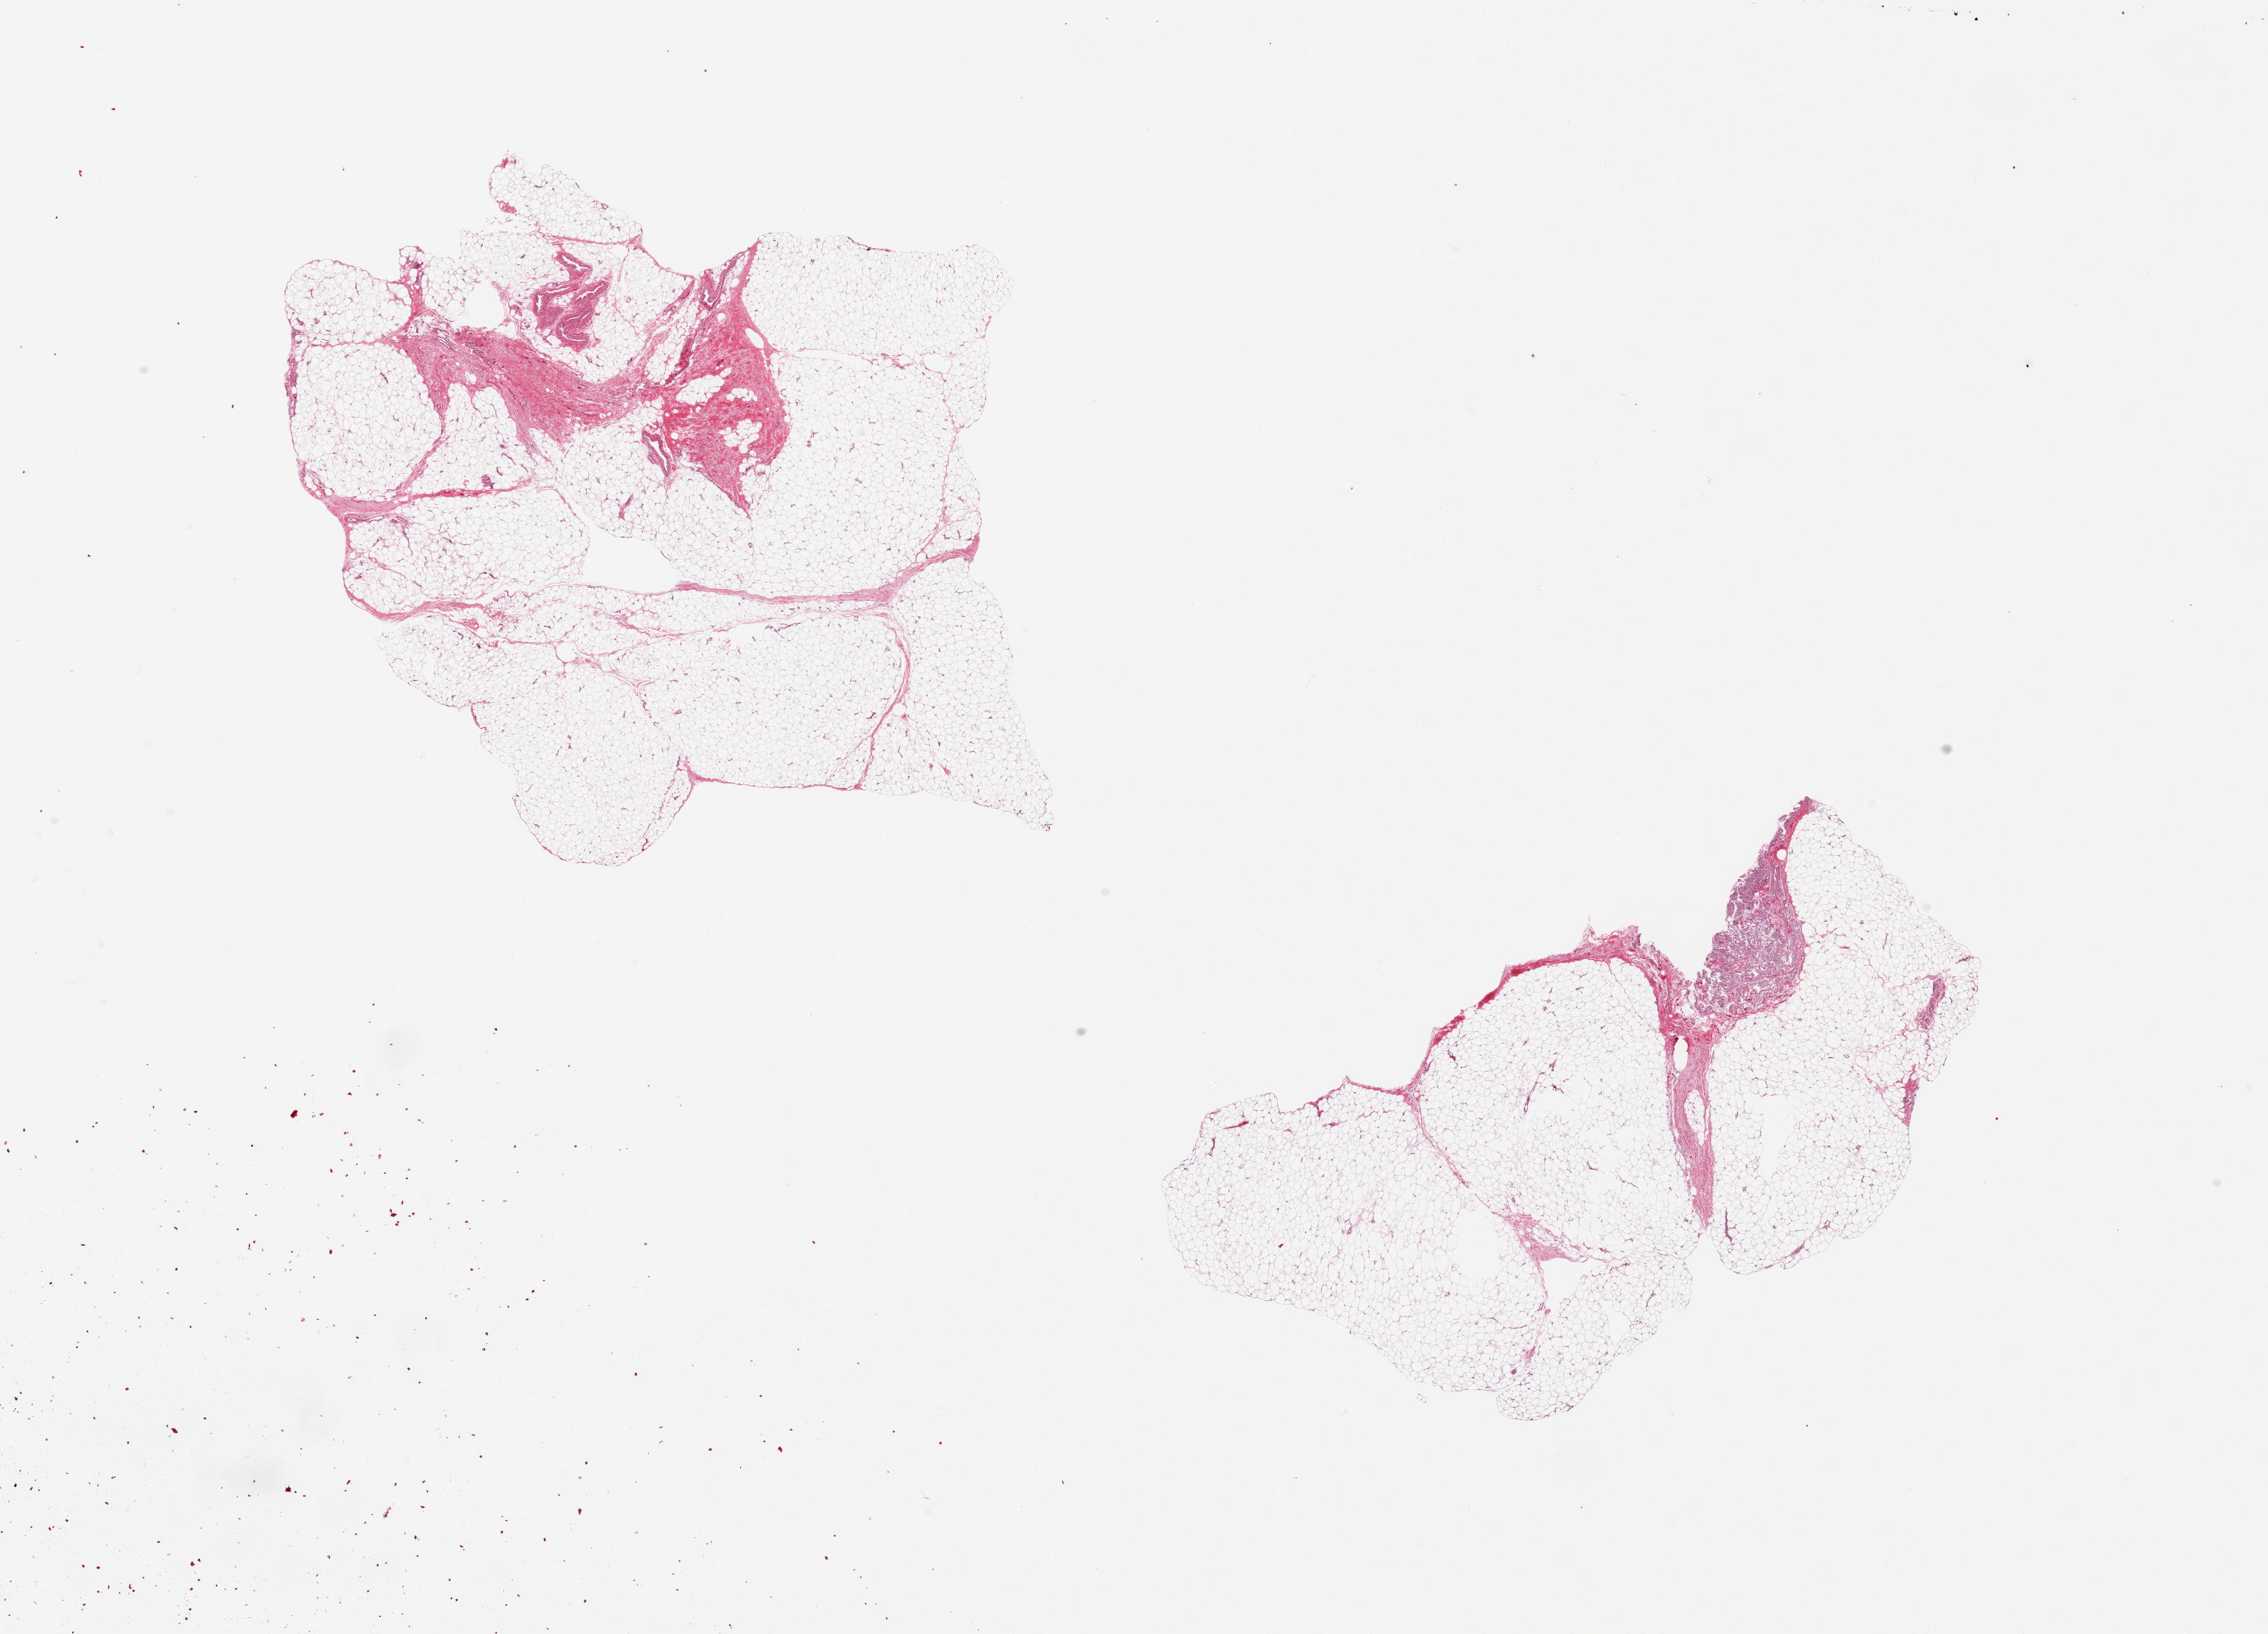
Digitized hematoxylin and eosin (H&E)-stained section, brightfield — low-resolution overview of the scanned area, about 25.6 x 18.4 mm (slide scanned at 20x), PAXgene-fixed paraffin-embedded (PFPE) section, target tissue: adipose tissue, tissue donor sample. Donor: male.
* pathologist's review note for this sample: 2 pieces, ~8x6mm